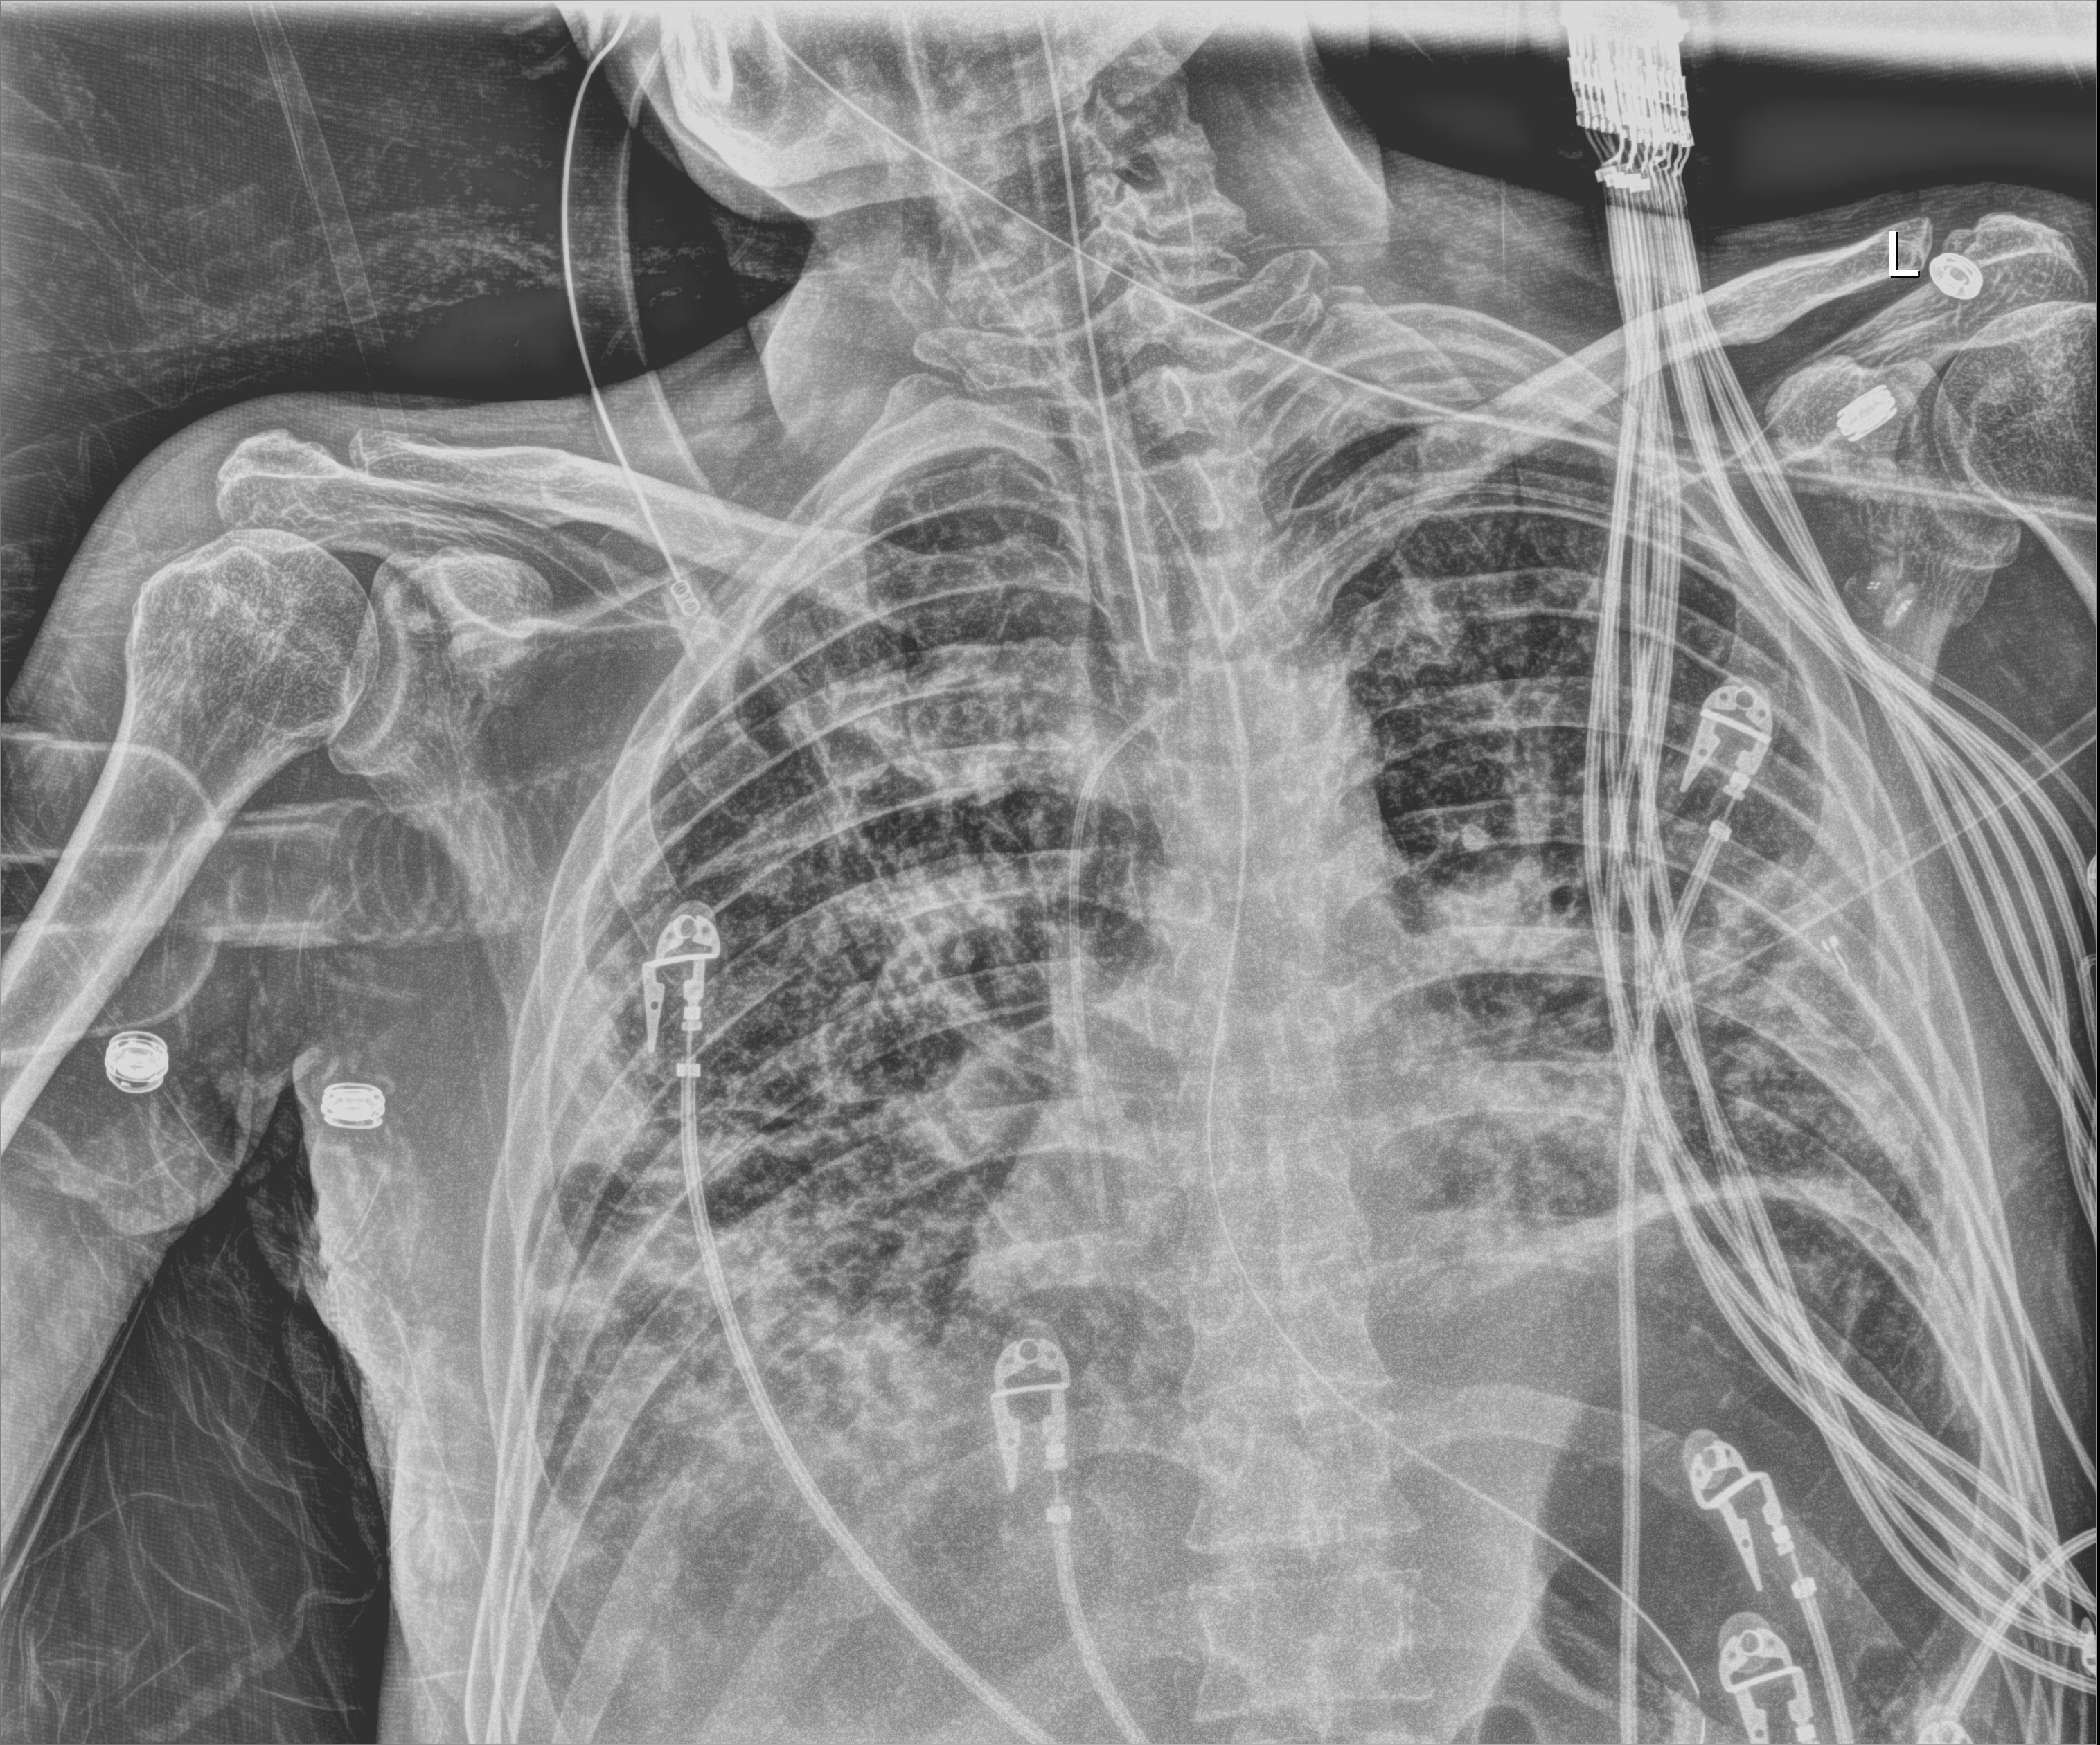
Chest radiograph (digital radiography); anteroposterior (AP) projection. Male patient hospitalised with COVID-19, age 18–59 years.
Hospital-stay facts (about this admission, not read from this image; timing relative to this image not recorded): diabetes (admission record): yes.